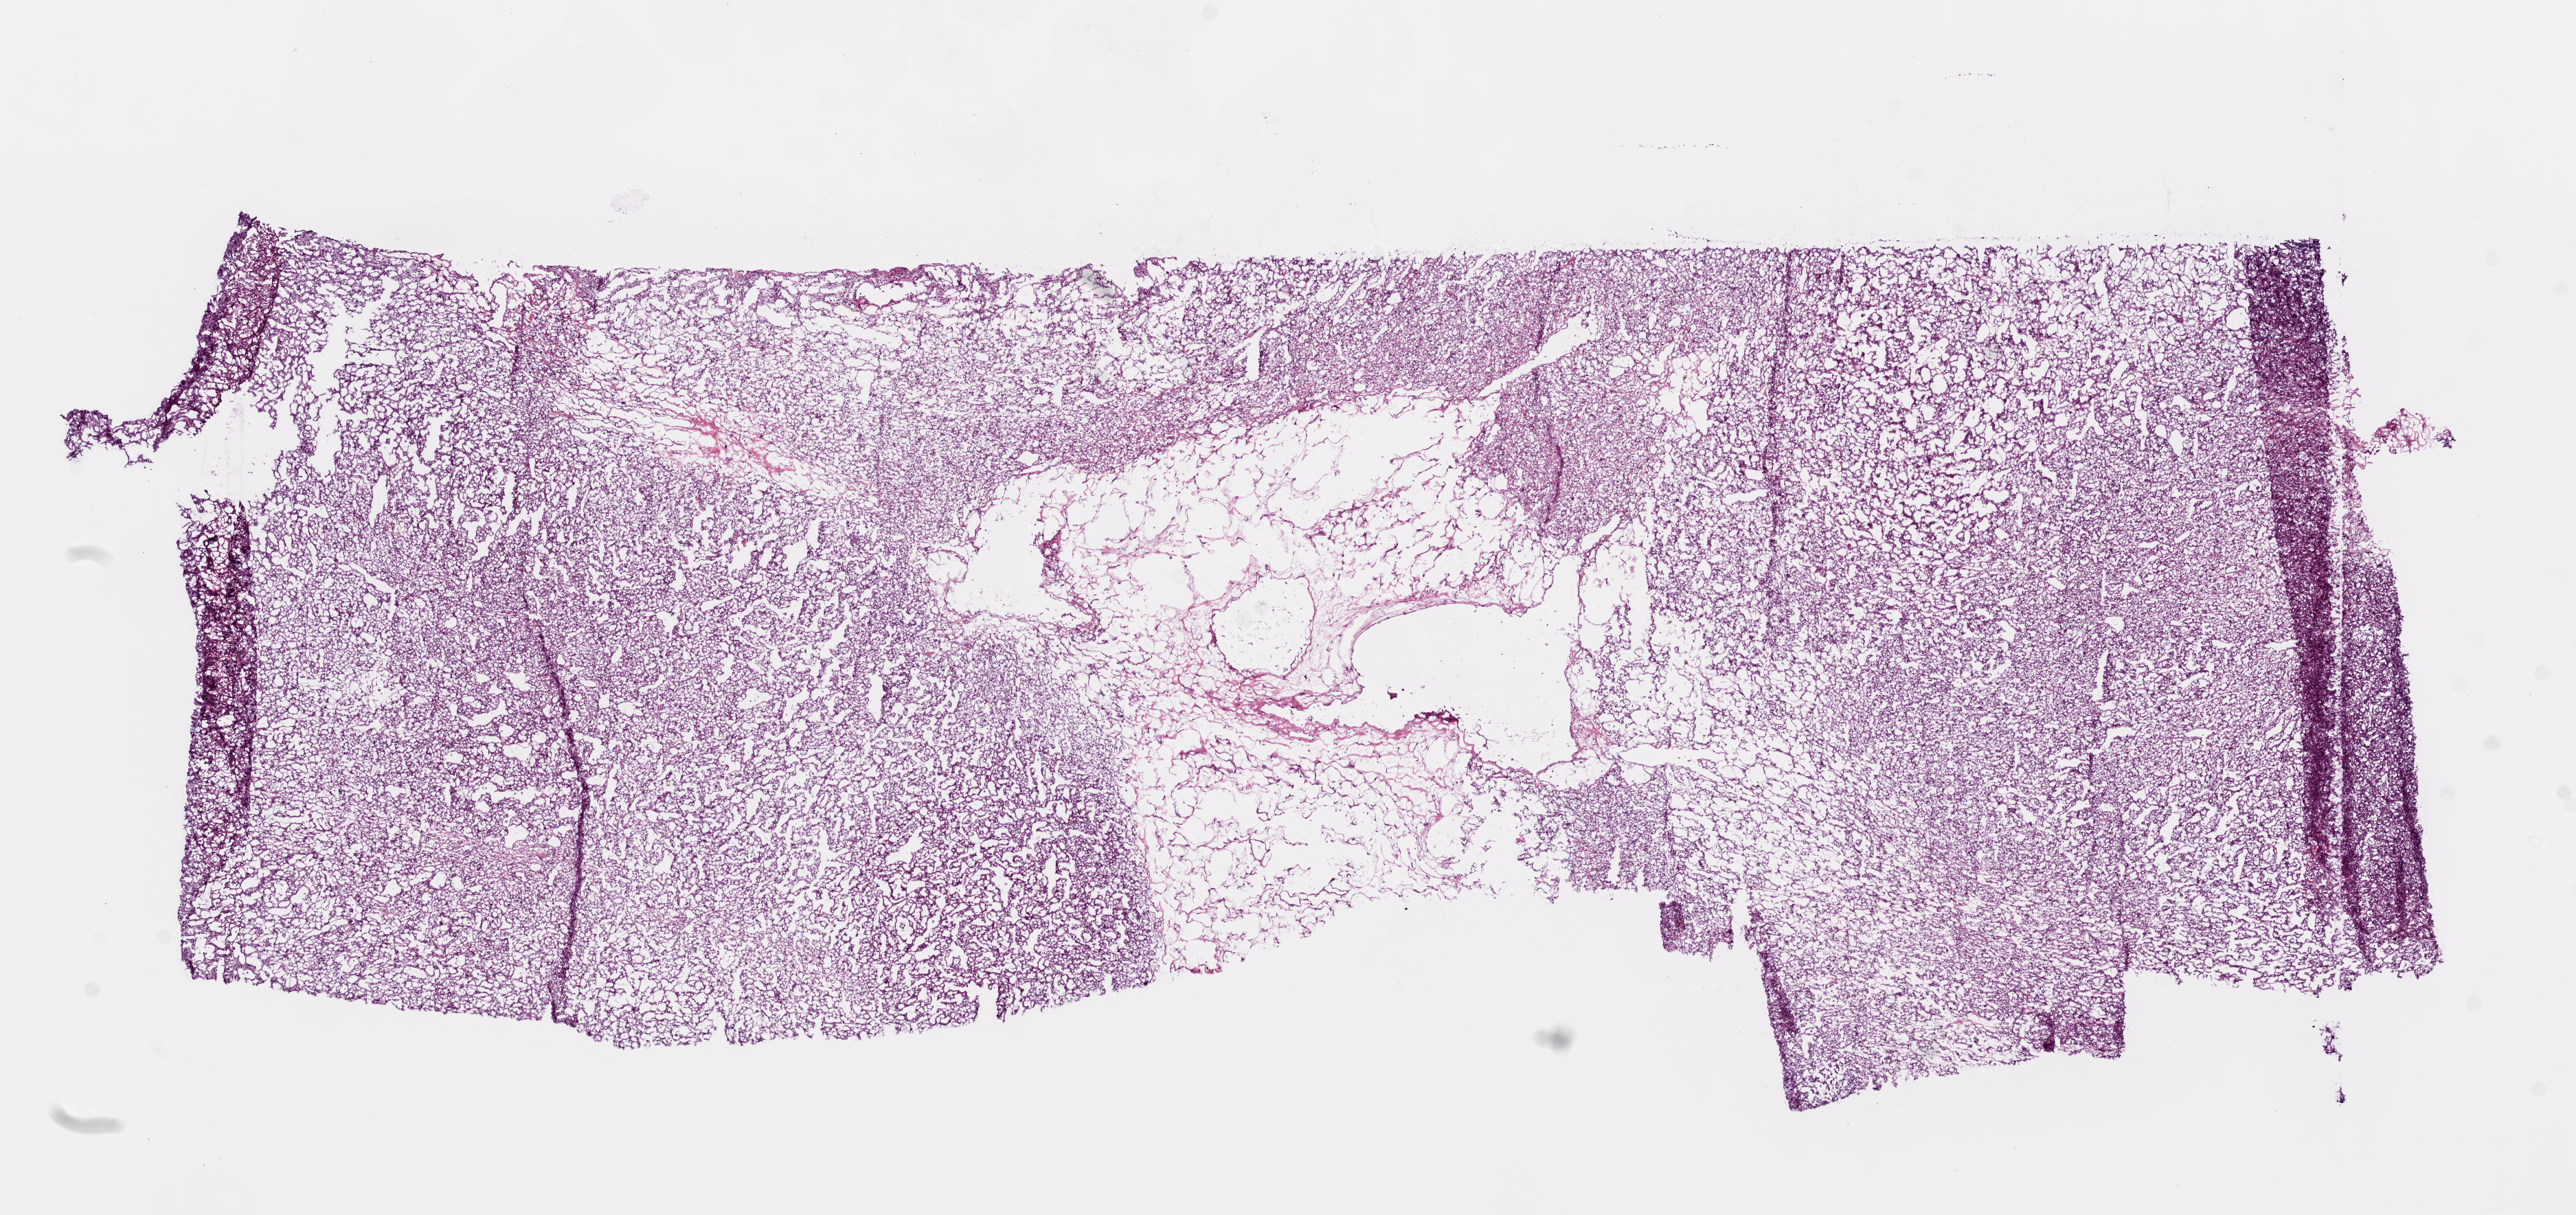
Hematoxylin and eosin (H&E) stained whole-slide image, a low-resolution overview of the entire scanned area, about 15.0 x 7.1 mm (slide scanned at 20x), frozen section from the bottom of the tissue portion, primary tumour sample from the kidney. Patient: female, age at initial diagnosis 68 years. Histologic grade: G3 (poorly differentiated). Slide review estimates, as recorded: tumour cells 75%, tumour nuclei 80%, normal cells 0%, stromal cells 25%, necrosis 0%.
* histologic diagnosis: Clear cell adenocarcinoma, NOS
* AJCC pathologic stage: IV
* TNM: T2 N0 M1